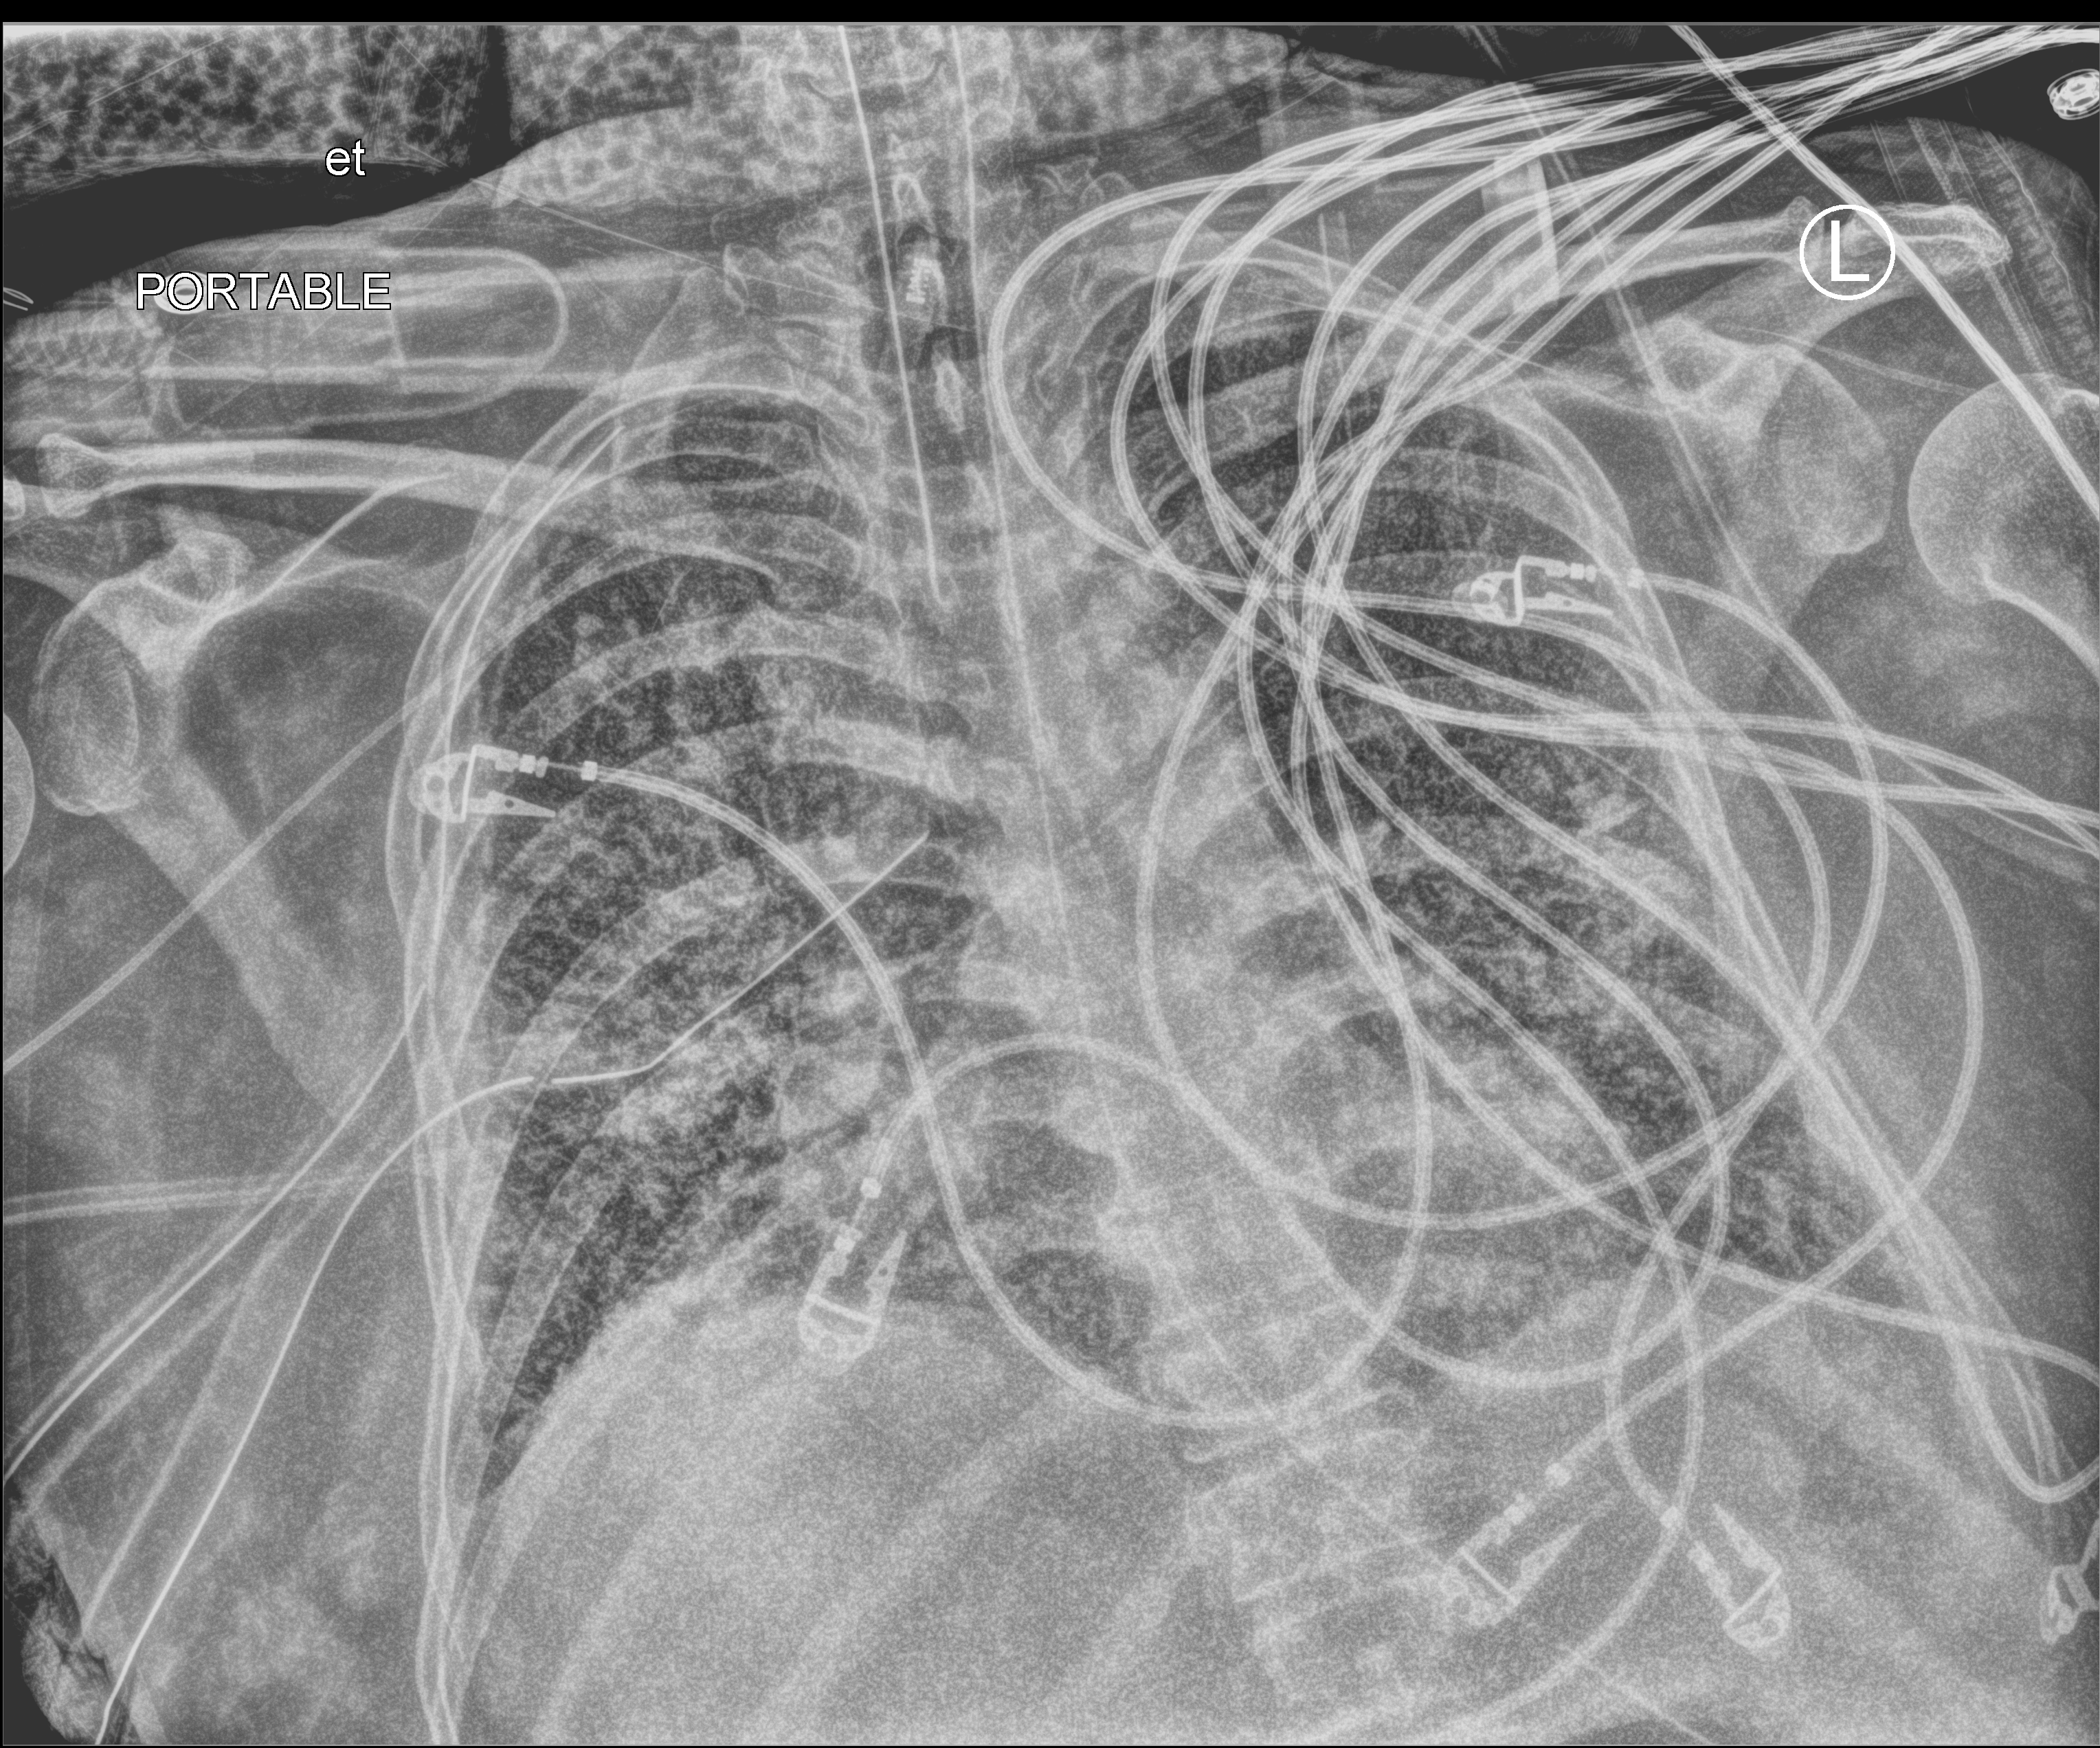
Chest X-ray (portable), anteroposterior (AP) projection. Adult patient hospitalised with COVID-19, age 18–59 years.
From the hospital-stay record, not from the radiograph (when in the stay this image was taken is not recorded):
- hypertension (admission record): no
- admitted to intensive care during this hospital stay: yes